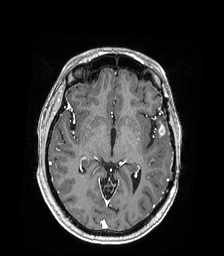
Brain MRI from a brain-tumour surgery series, one axial slice. Slice 106 of 168 in the series (ordered by position). T1-weighted post-contrast. 1 mm slice thickness. 224 × 256 image matrix, field of view 224 × 256 mm. Case-level facts recorded for this patient, not image findings: histopathology: Astrocytoma; WHO grade: 4; IDH mutation: yes; tumour location: Left Temporal.
Annotated regions visible in this slice (outlined manually by an expert reader):
- tumour: bounding box (x1, y1, x2, y2) in pixels: (151, 123, 158, 137)